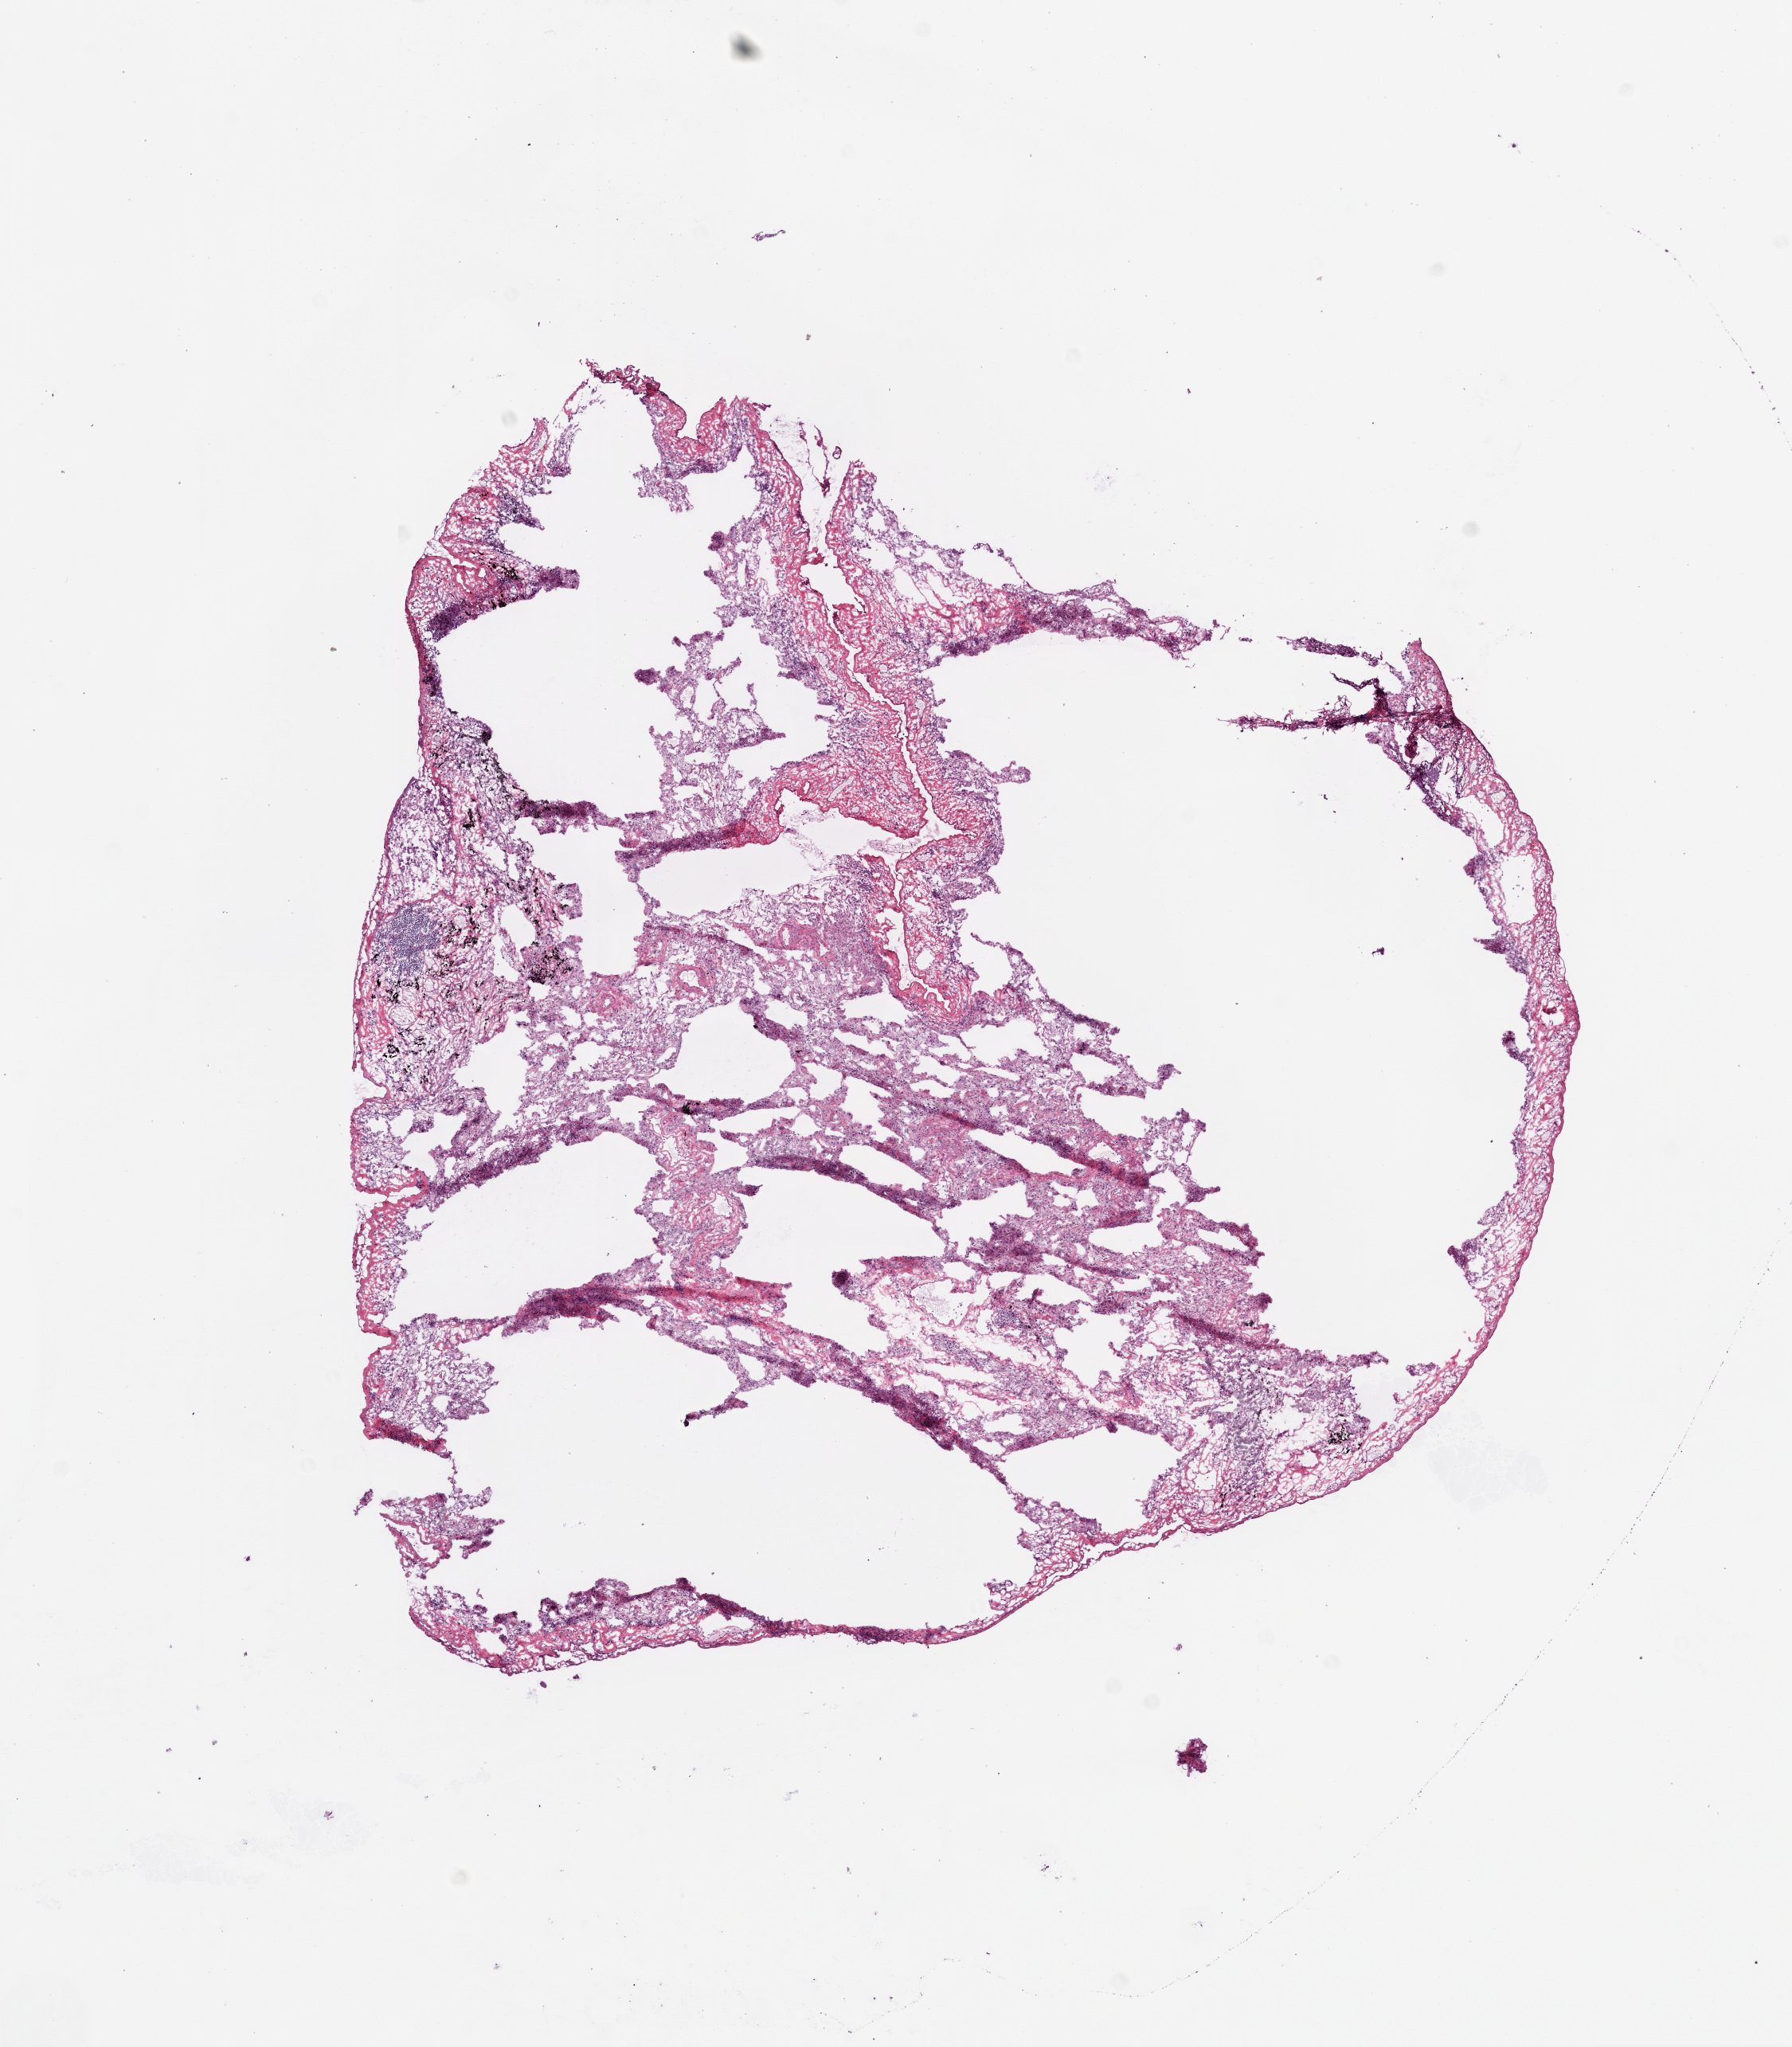
Digitized Hematoxylin and eosin (H&E) stained tissue section (whole slide), shown as a low-resolution overview of the whole scanned area (about 9.0 x 10.3 mm, acquisition: 20x scan). Frozen section. Sample: solid tissue normal (non-tumour tissue), lung. Female, age 55 years at initial diagnosis.
This section: solid tissue normal (non-tumour) sample from the same patient. Patient diagnosis: Squamous cell carcinoma, NOS (lower lobe, lung).